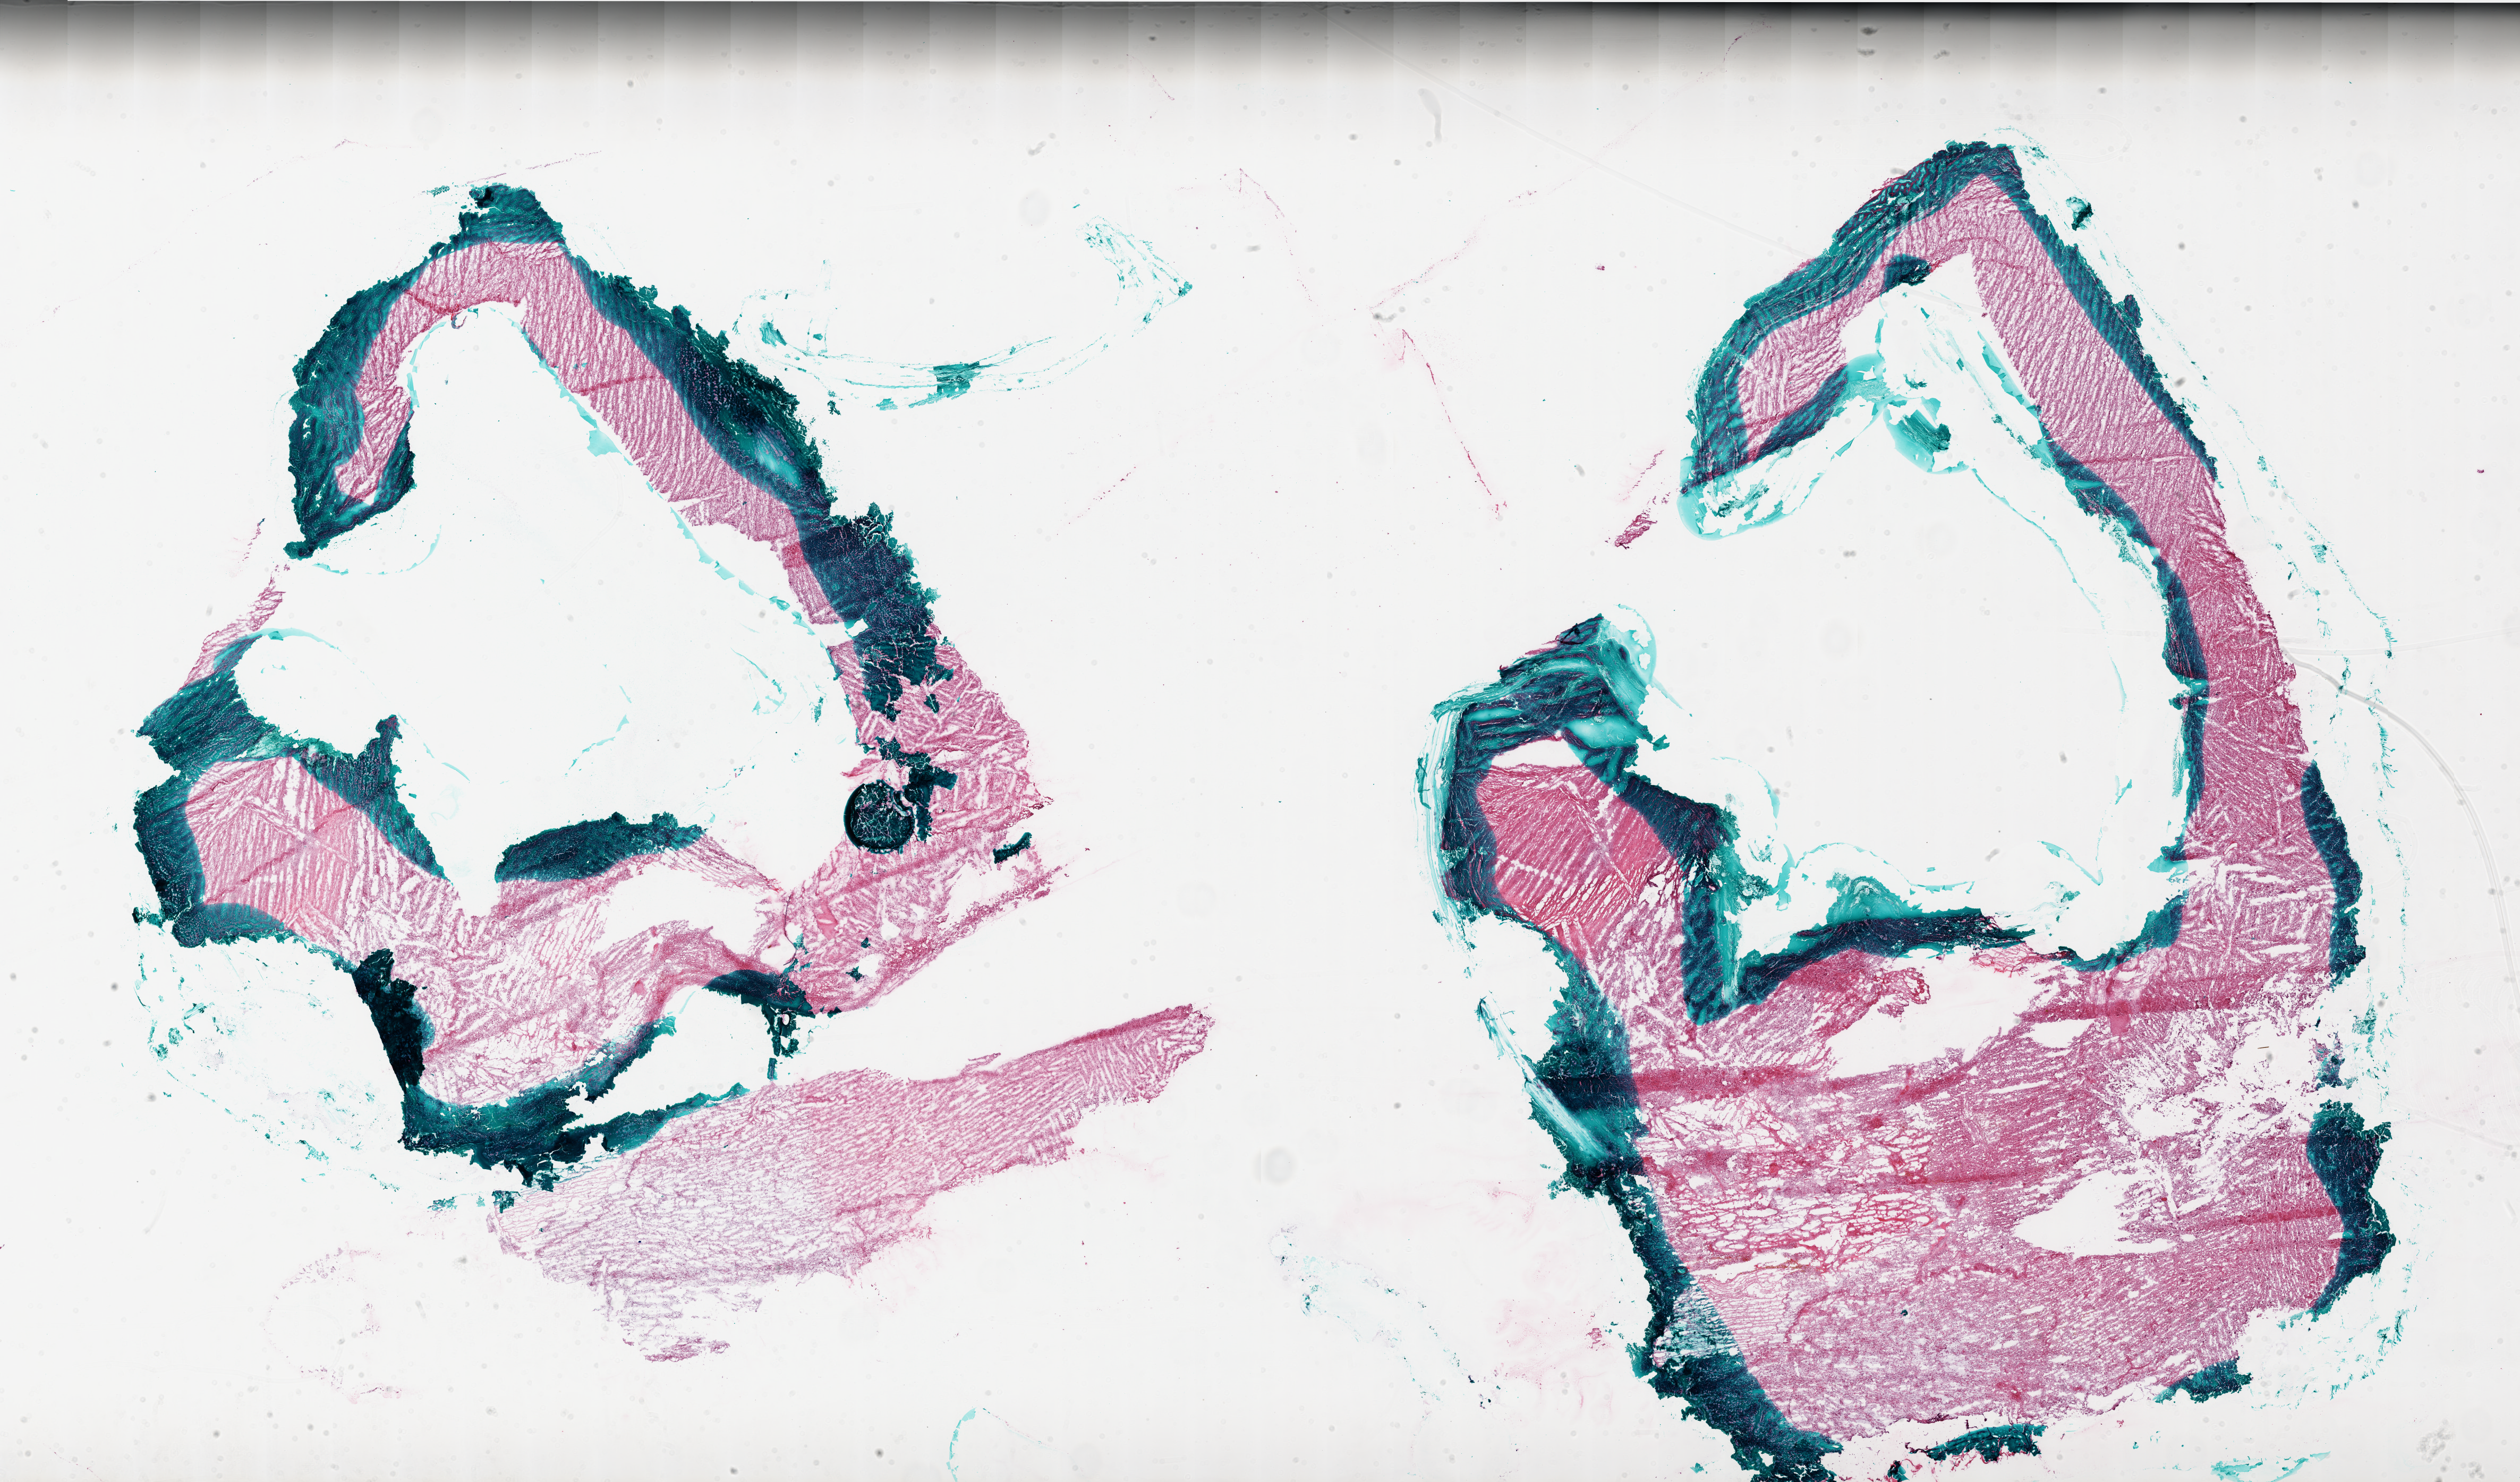
H&E whole-slide image — whole scanned area (about 38.0 x 22.3 mm) shown as a low-resolution overview, frozen section from the bottom of the tissue portion, sample: primary tumour, brain. Female patient; age at initial diagnosis 66 years. Slide review estimates, as recorded: tumour cells 75%, tumour nuclei 95%, normal cells 0%, stromal cells 10%, necrosis 15%.
Diagnosis: Glioblastoma.